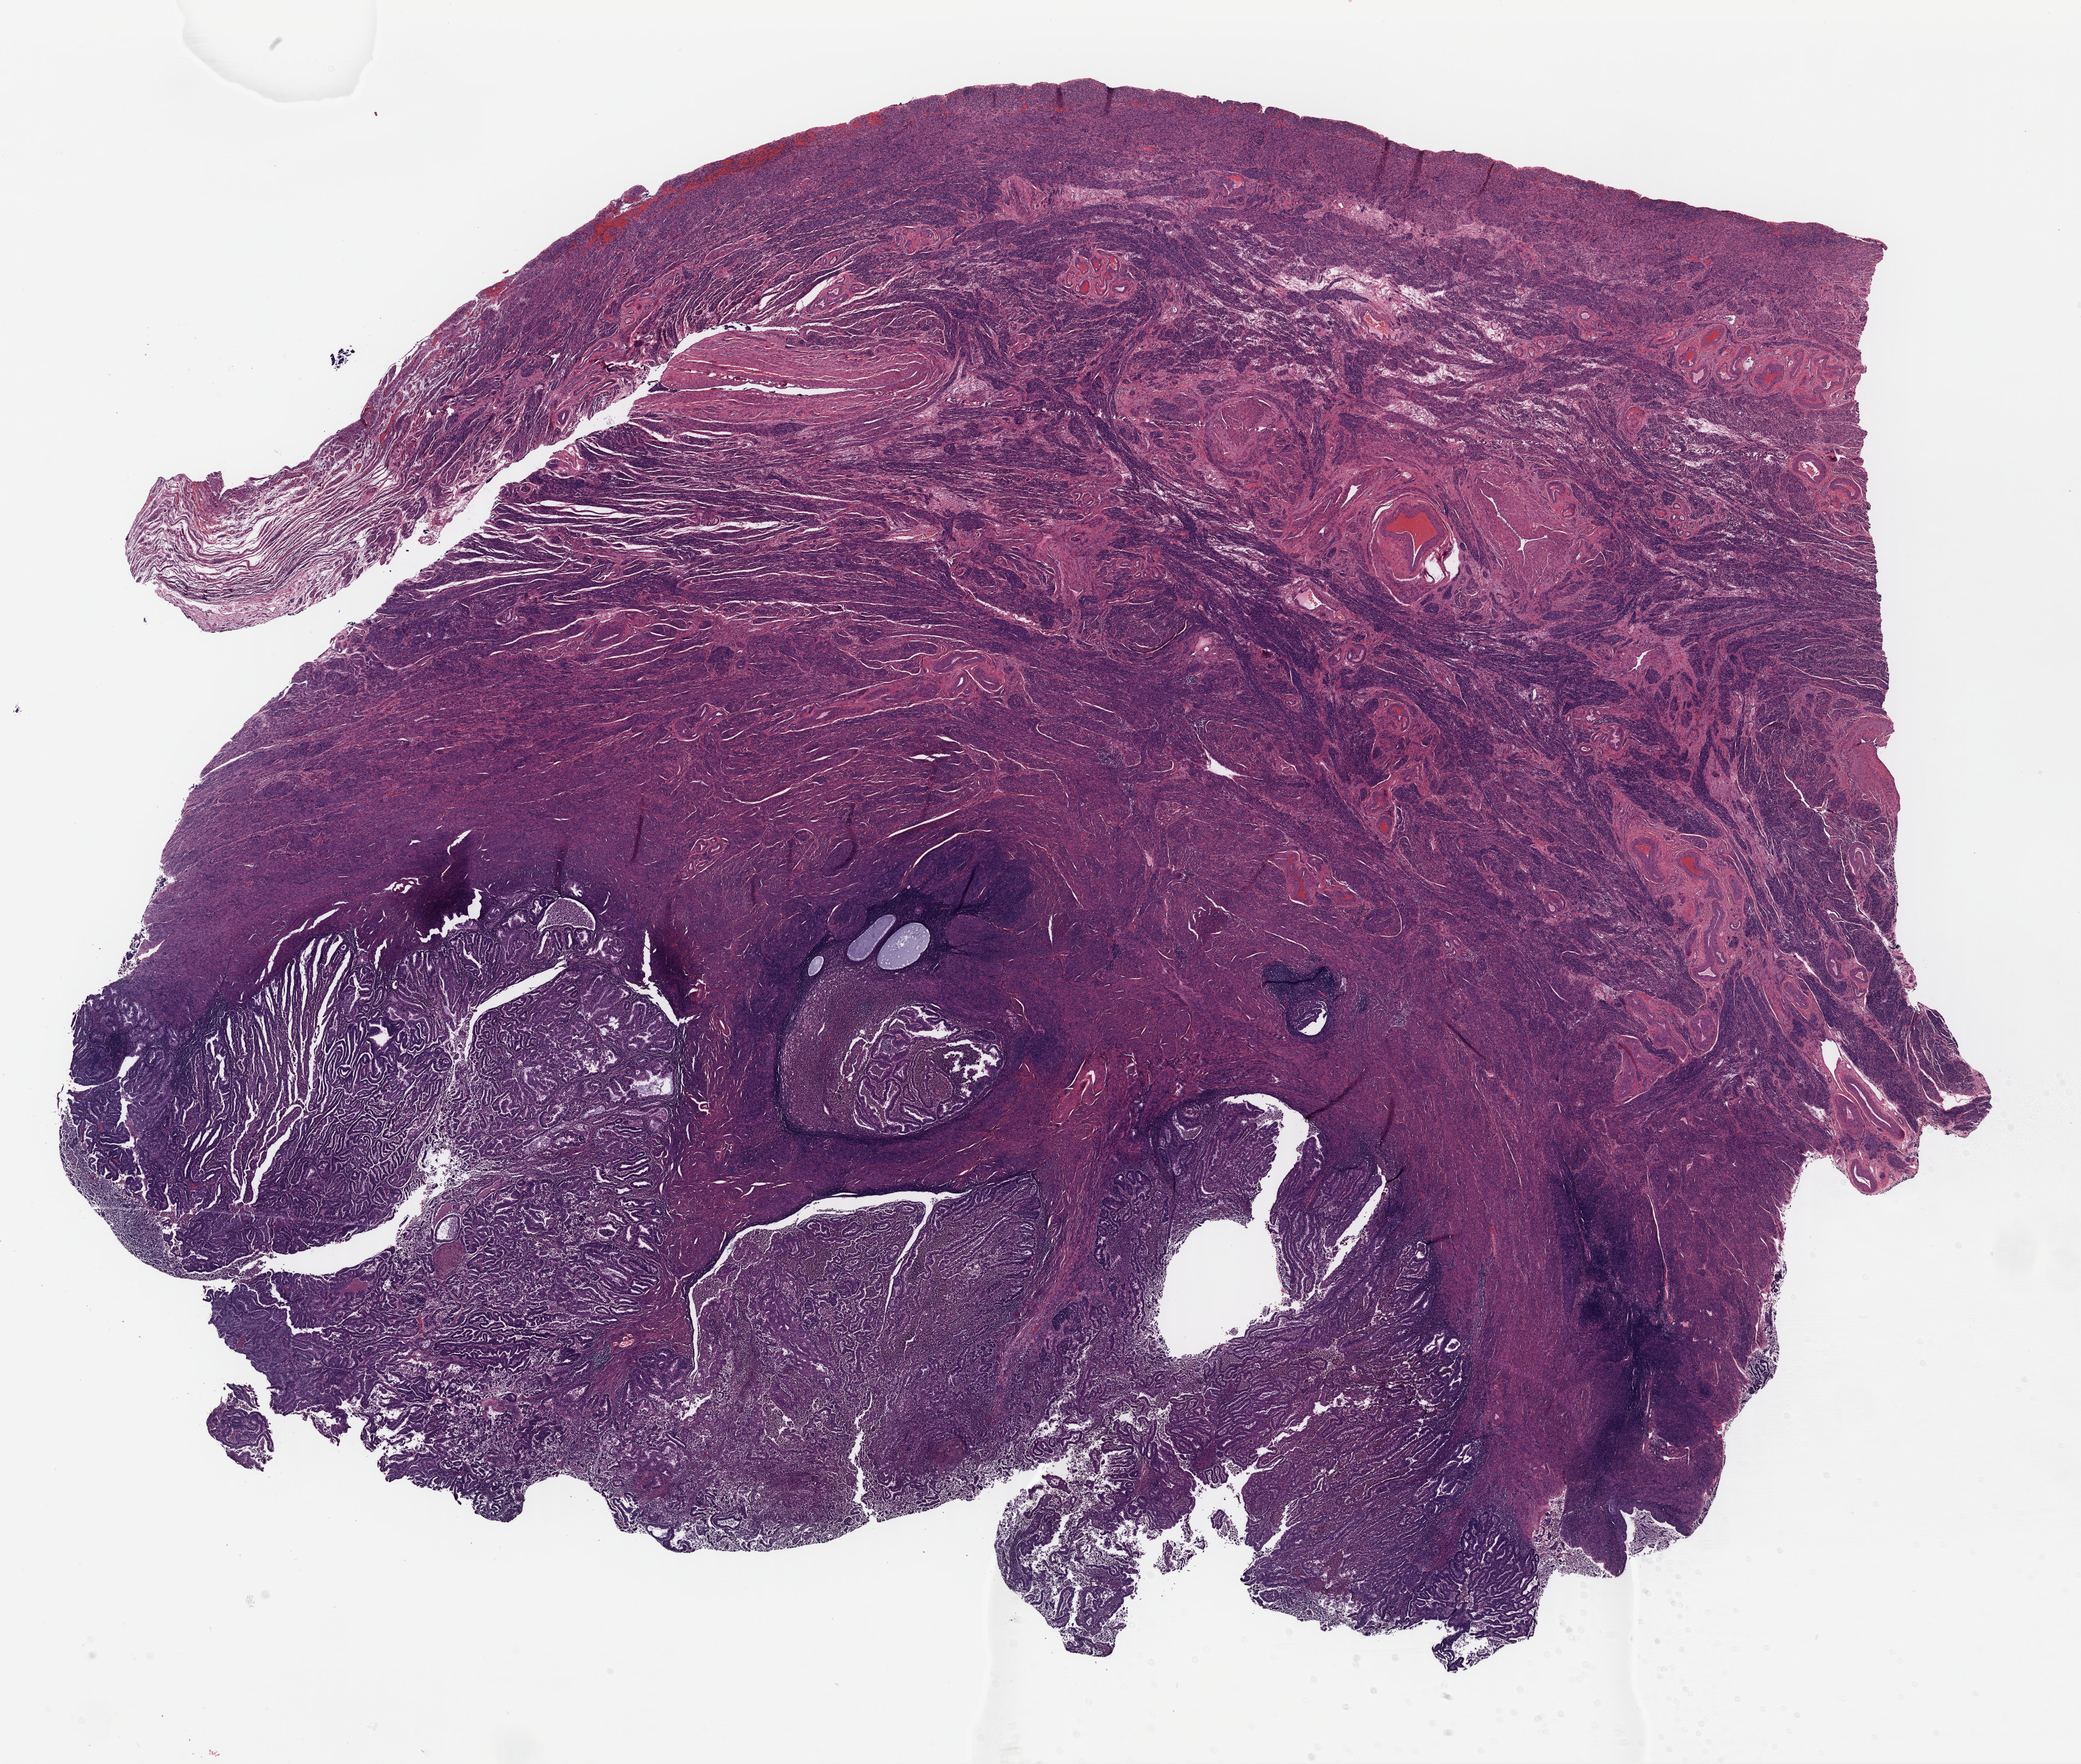
Digitized H&E tissue section (whole slide) — shown as a low-resolution overview of the whole scanned area (about 25.3 x 21.4 mm, acquisition: 40x scan), formalin-fixed paraffin-embedded (FFPE) diagnostic section, sample: primary tumour, uterus. Female patient; age at initial diagnosis 68 years. Histologic grade: G3 (poorly differentiated).
Histologic diagnosis: Endometrioid adenocarcinoma, NOS (endometrium). FIGO stage: IA.